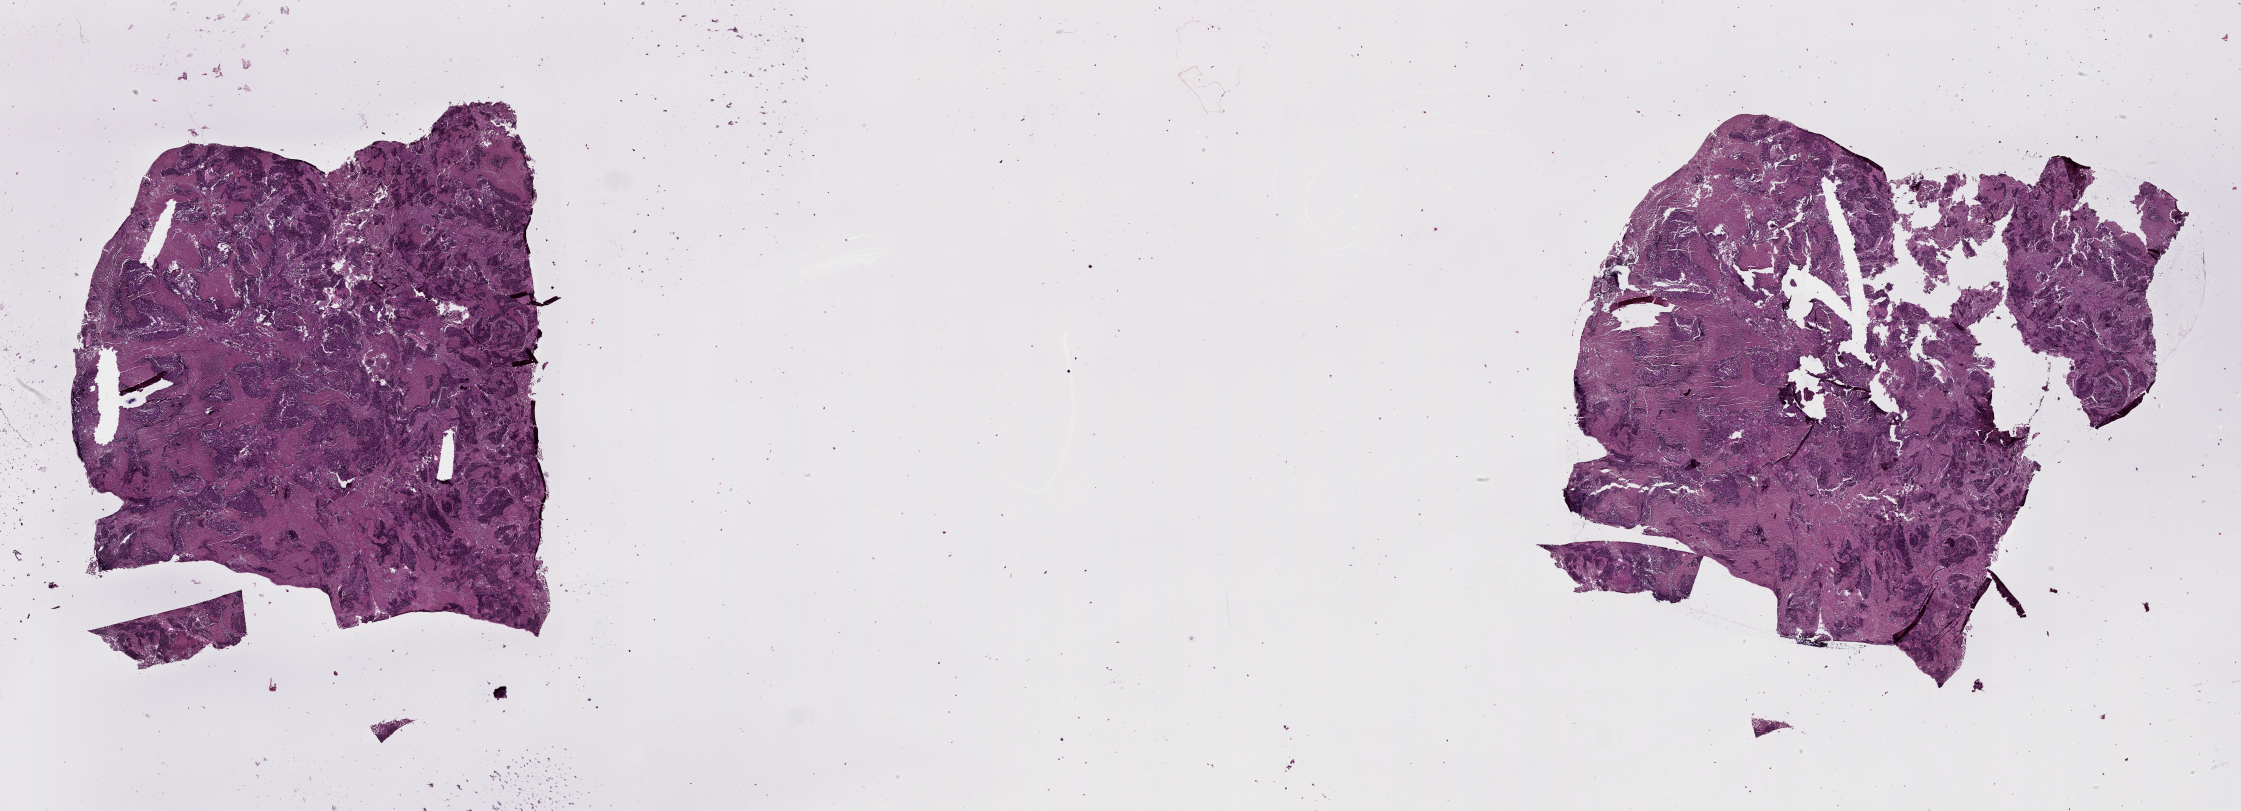
Digitized Hematoxylin and eosin (H&E) stained tissue section (whole slide) — shown as a low-resolution overview of the whole scanned area (about 36.1 x 13.1 mm); lung, tumour tissue. Male, 68 y/o.
Patient diagnosis (cohort enrolment): squamous cell carcinoma (lung).